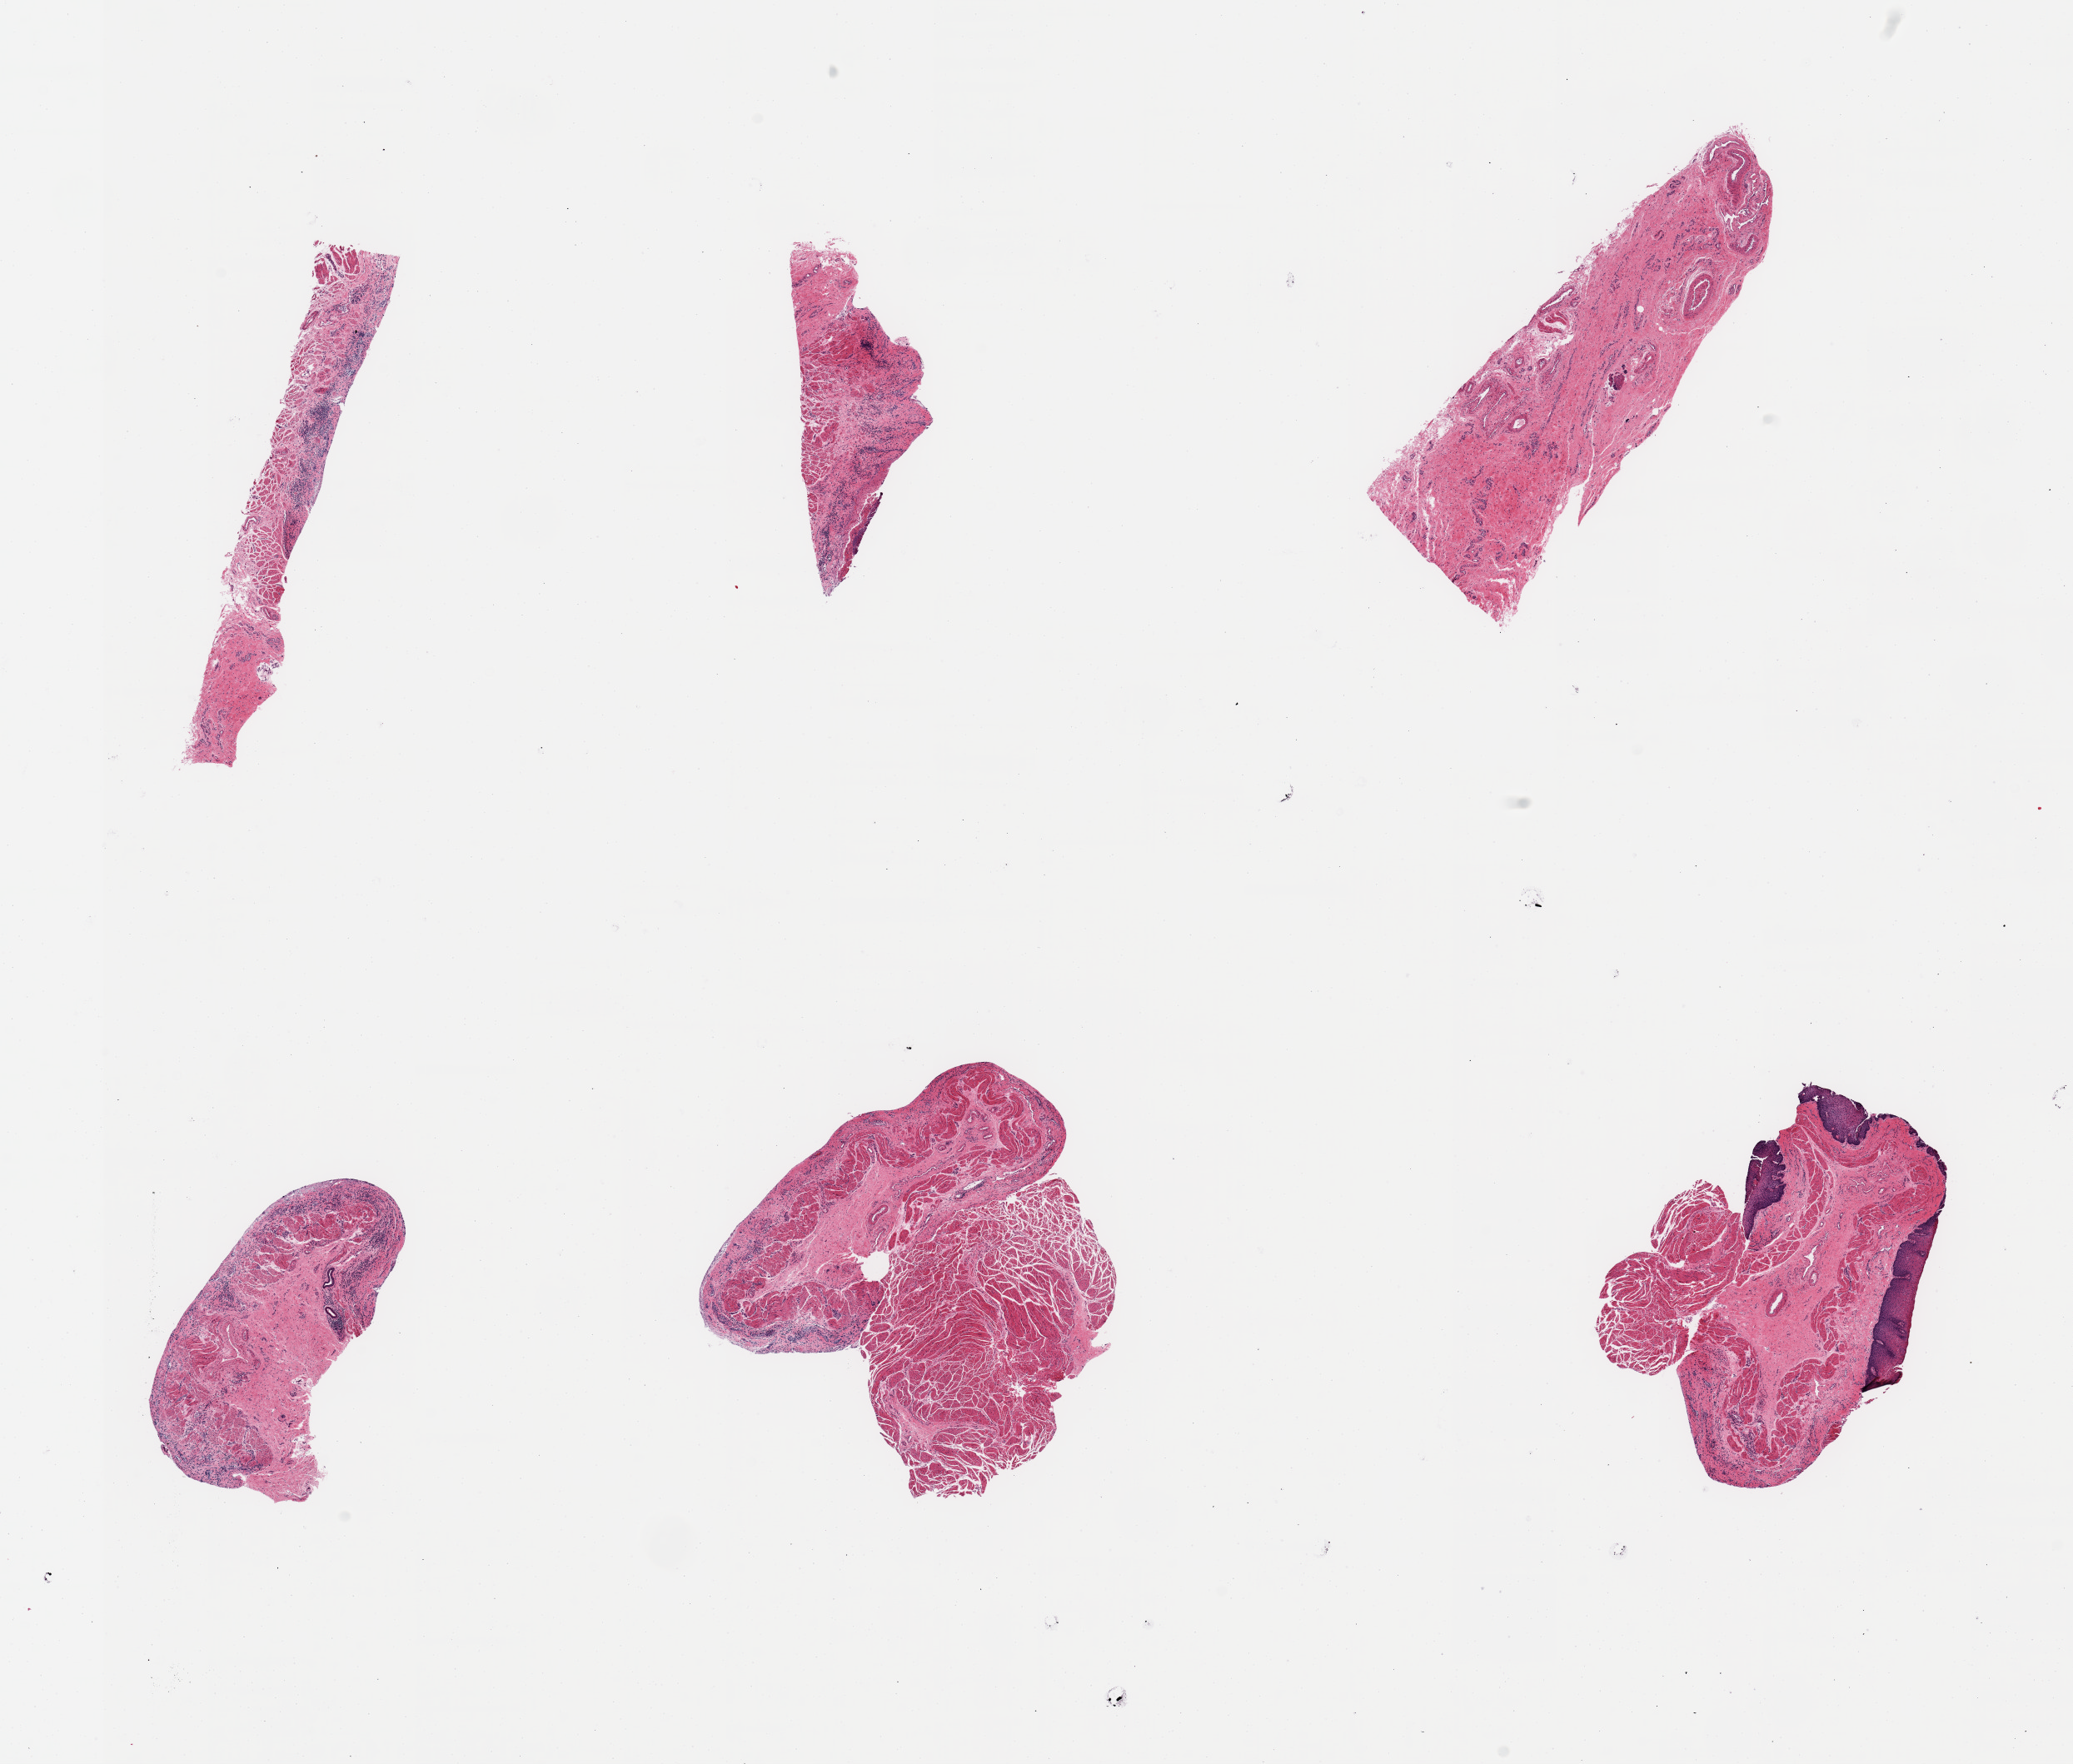
Digitized H&E-stained section, brightfield, a low-resolution overview of the entire scanned area, about 19.7 x 16.8 mm, PAXgene-fixed, paraffin-embedded tissue, target tissue: esophageal mucous membrane, donor tissue sample. Donor: female.
* pathologist's review note for this sample: 6 pieces; only one piece contains a trace of target stratified squamous epithelium; submucosa and muscularis included